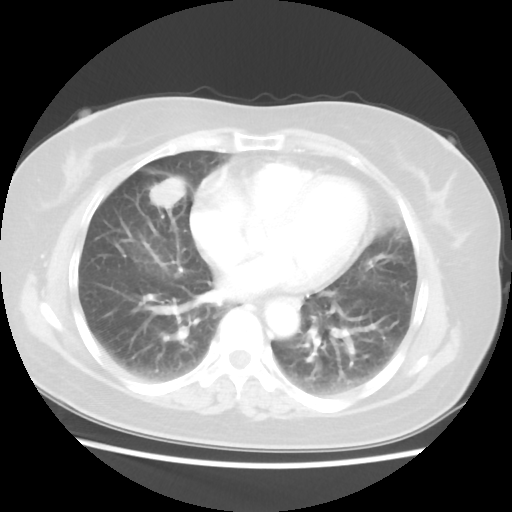
Chest CT, one axial slice. Slice 21 of 48 in the series (ordered by position). Reconstruction kernel STANDARD. Lung window (W 1500 / L -600 HU). 512 × 512 image matrix, field of view 343 × 343 mm. Female patient, age 61 years. From the clinical record (not read from this slice): clinical TNM (as recorded): T1c N0 M0.
Structures marked on this image (rectangle marked by the reading radiologist):
- lung tumour (recorded histology: adenocarcinoma): box from (x=145, y=174) to (x=186, y=215) px